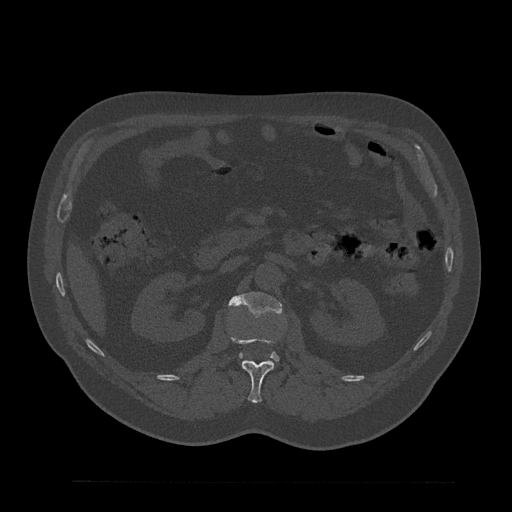
CT including the spine, one axial slice. Slice 140 of 797 in the series (ordered by position). Reconstruction kernel Br40s/3. Bone window (W 1800 / L 400 HU). 512 × 512 image matrix, field of view 430 × 430 mm. Patient: male, 61 years. From the clinical record (not read from this slice): primary cancer: prostate.
Annotated regions visible in this slice (semi-automatic segmentation, software-assisted and operator-edited):
- L1 vertebra: box from (x=230, y=335) to (x=275, y=403) px
- L2 vertebra: (x=228, y=292)–(x=282, y=360)